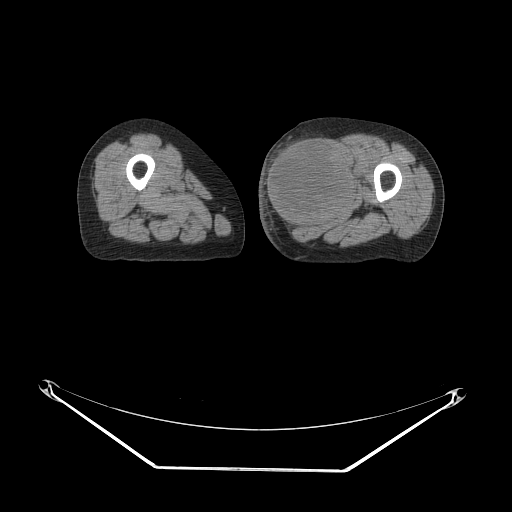
CT of an extremity soft-tissue mass (from a PET/CT study), one axial slice; slice 31 of 91 in the series (ordered by position); reconstruction kernel STANDARD; soft-tissue window (W 400 / L 40 HU); 512 × 512 image matrix, field of view 500 × 500 mm. Female patient. Case-level facts recorded for this patient, not image findings: histological type: pleomorphic leiomyosarcoma; grade: high; site of the primary tumour: left thigh.
Annotated regions visible in this slice (expert contour drawn on MRI and transferred to this co-registered scan by the dataset authors):
- gross tumour volume including surrounding oedema: box from (x=265, y=133) to (x=355, y=229) px
- gross tumour volume (mass): (x=265, y=135)–(x=355, y=227)